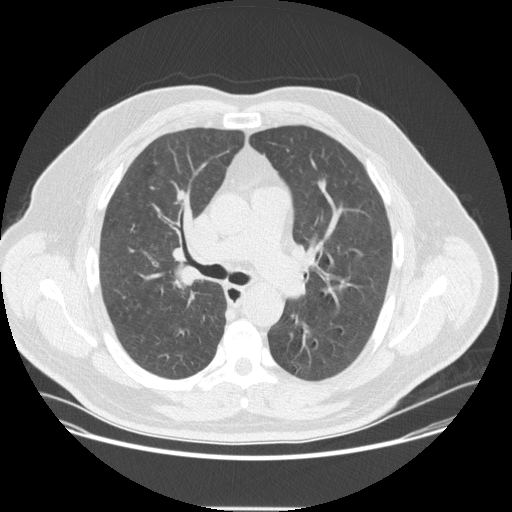
Low-dose screening chest CT, one axial slice; slice 223 of 351 in the series (ordered by position); 120 kVp; lung window (W 1500 / L -600 HU); 2.5 mm slice thickness; 512 × 512 image matrix, field of view 419 × 419 mm.
Outlined on this slice (manually delineated by an expert):
- lesion 1 (tumor, upper lobe of right lung): box from (x=174, y=271) to (x=201, y=288) px